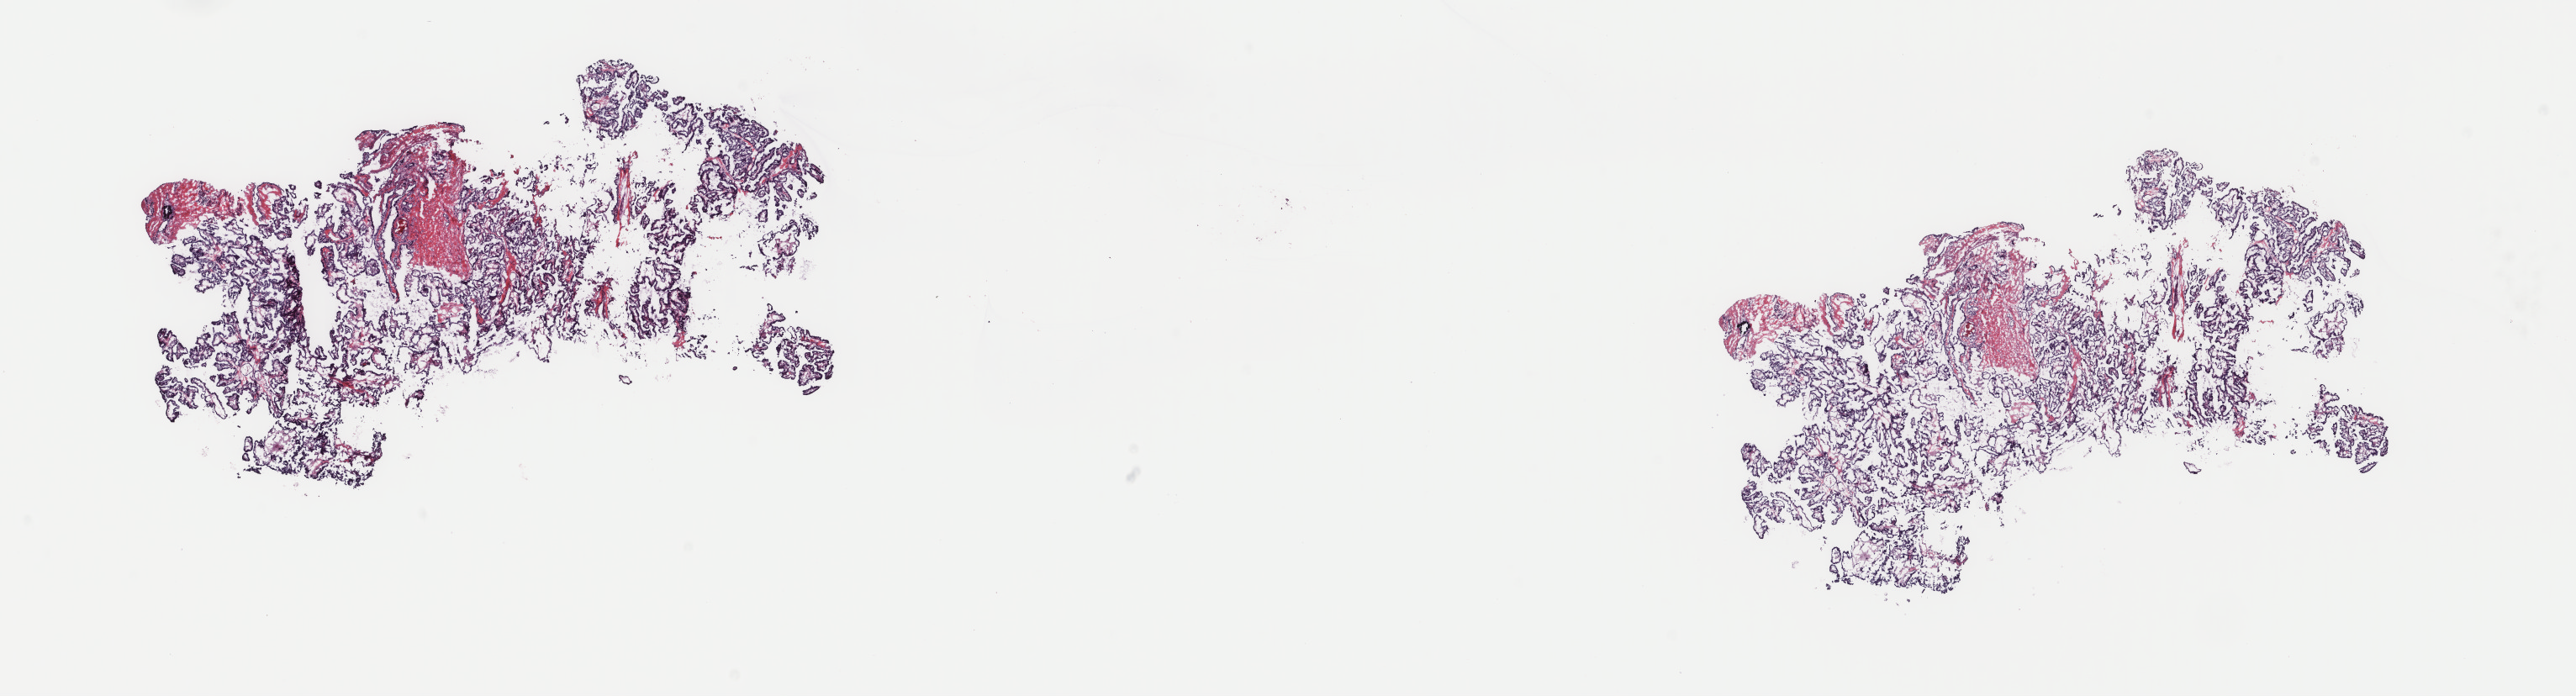
H&E whole-slide image — whole scanned area (about 24.3 x 6.6 mm) shown as a low-resolution overview. Frozen section. Thyroid, primary tumour sample. Patient: male, age at initial diagnosis 39 years. Slide review estimates, as recorded: tumour cells 80%, tumour nuclei 100%, normal cells 0%, stromal cells 20%, necrosis 0%. Infiltration values recorded for this section: lymphocyte infiltration 0%, monocyte infiltration 2%, neutrophil infiltration 0%.
Diagnosis: Papillary adenocarcinoma, NOS (thyroid gland). Lymph nodes positive (case pathology): 13 of 40 examined. AJCC pathologic stage: I (7th edition). TNM: T3 N1b M0.